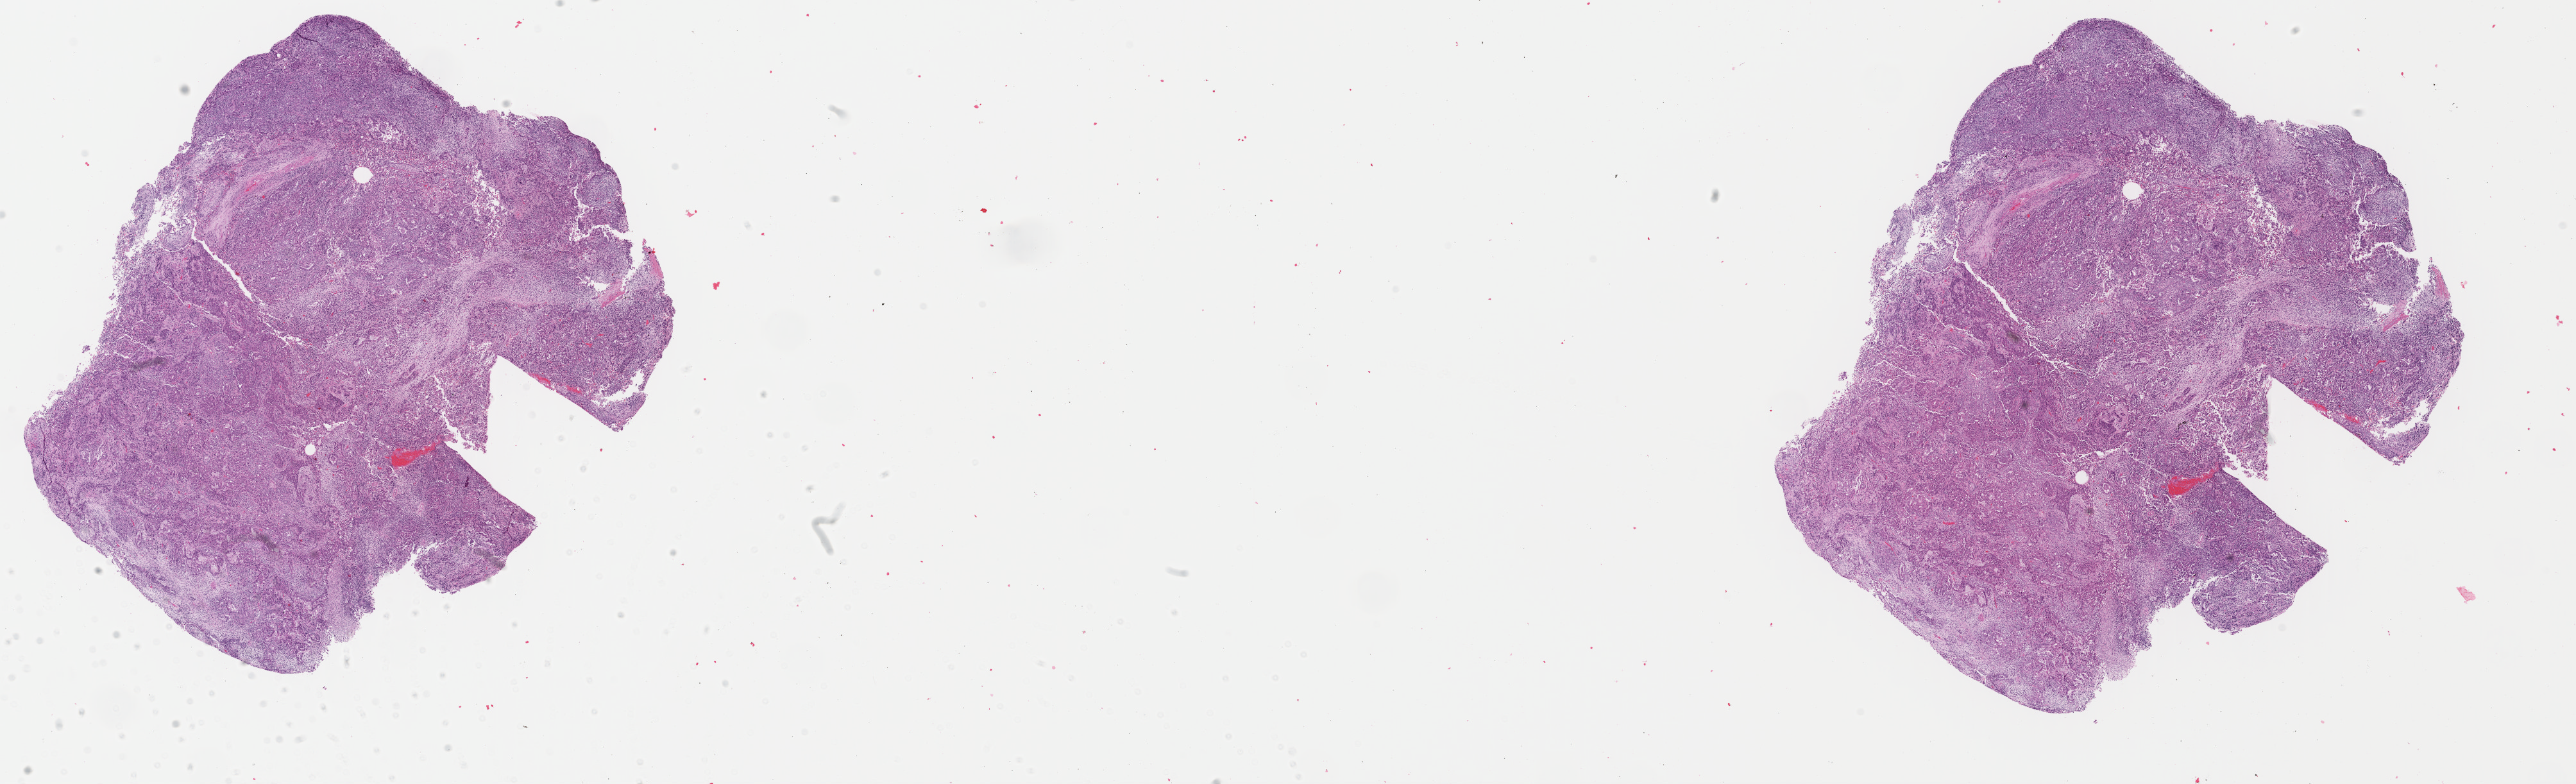
Digitized H&E tissue section (whole slide), low-resolution overview of the scanned area, about 31.7 x 9.6 mm (slide scanned at 40x), formalin-fixed paraffin-embedded (FFPE) diagnostic section, primary tumour sample from the uterus. Female, age 65 years at initial diagnosis.
* FIGO stage: IA
* histologic diagnosis: Mullerian mixed tumor